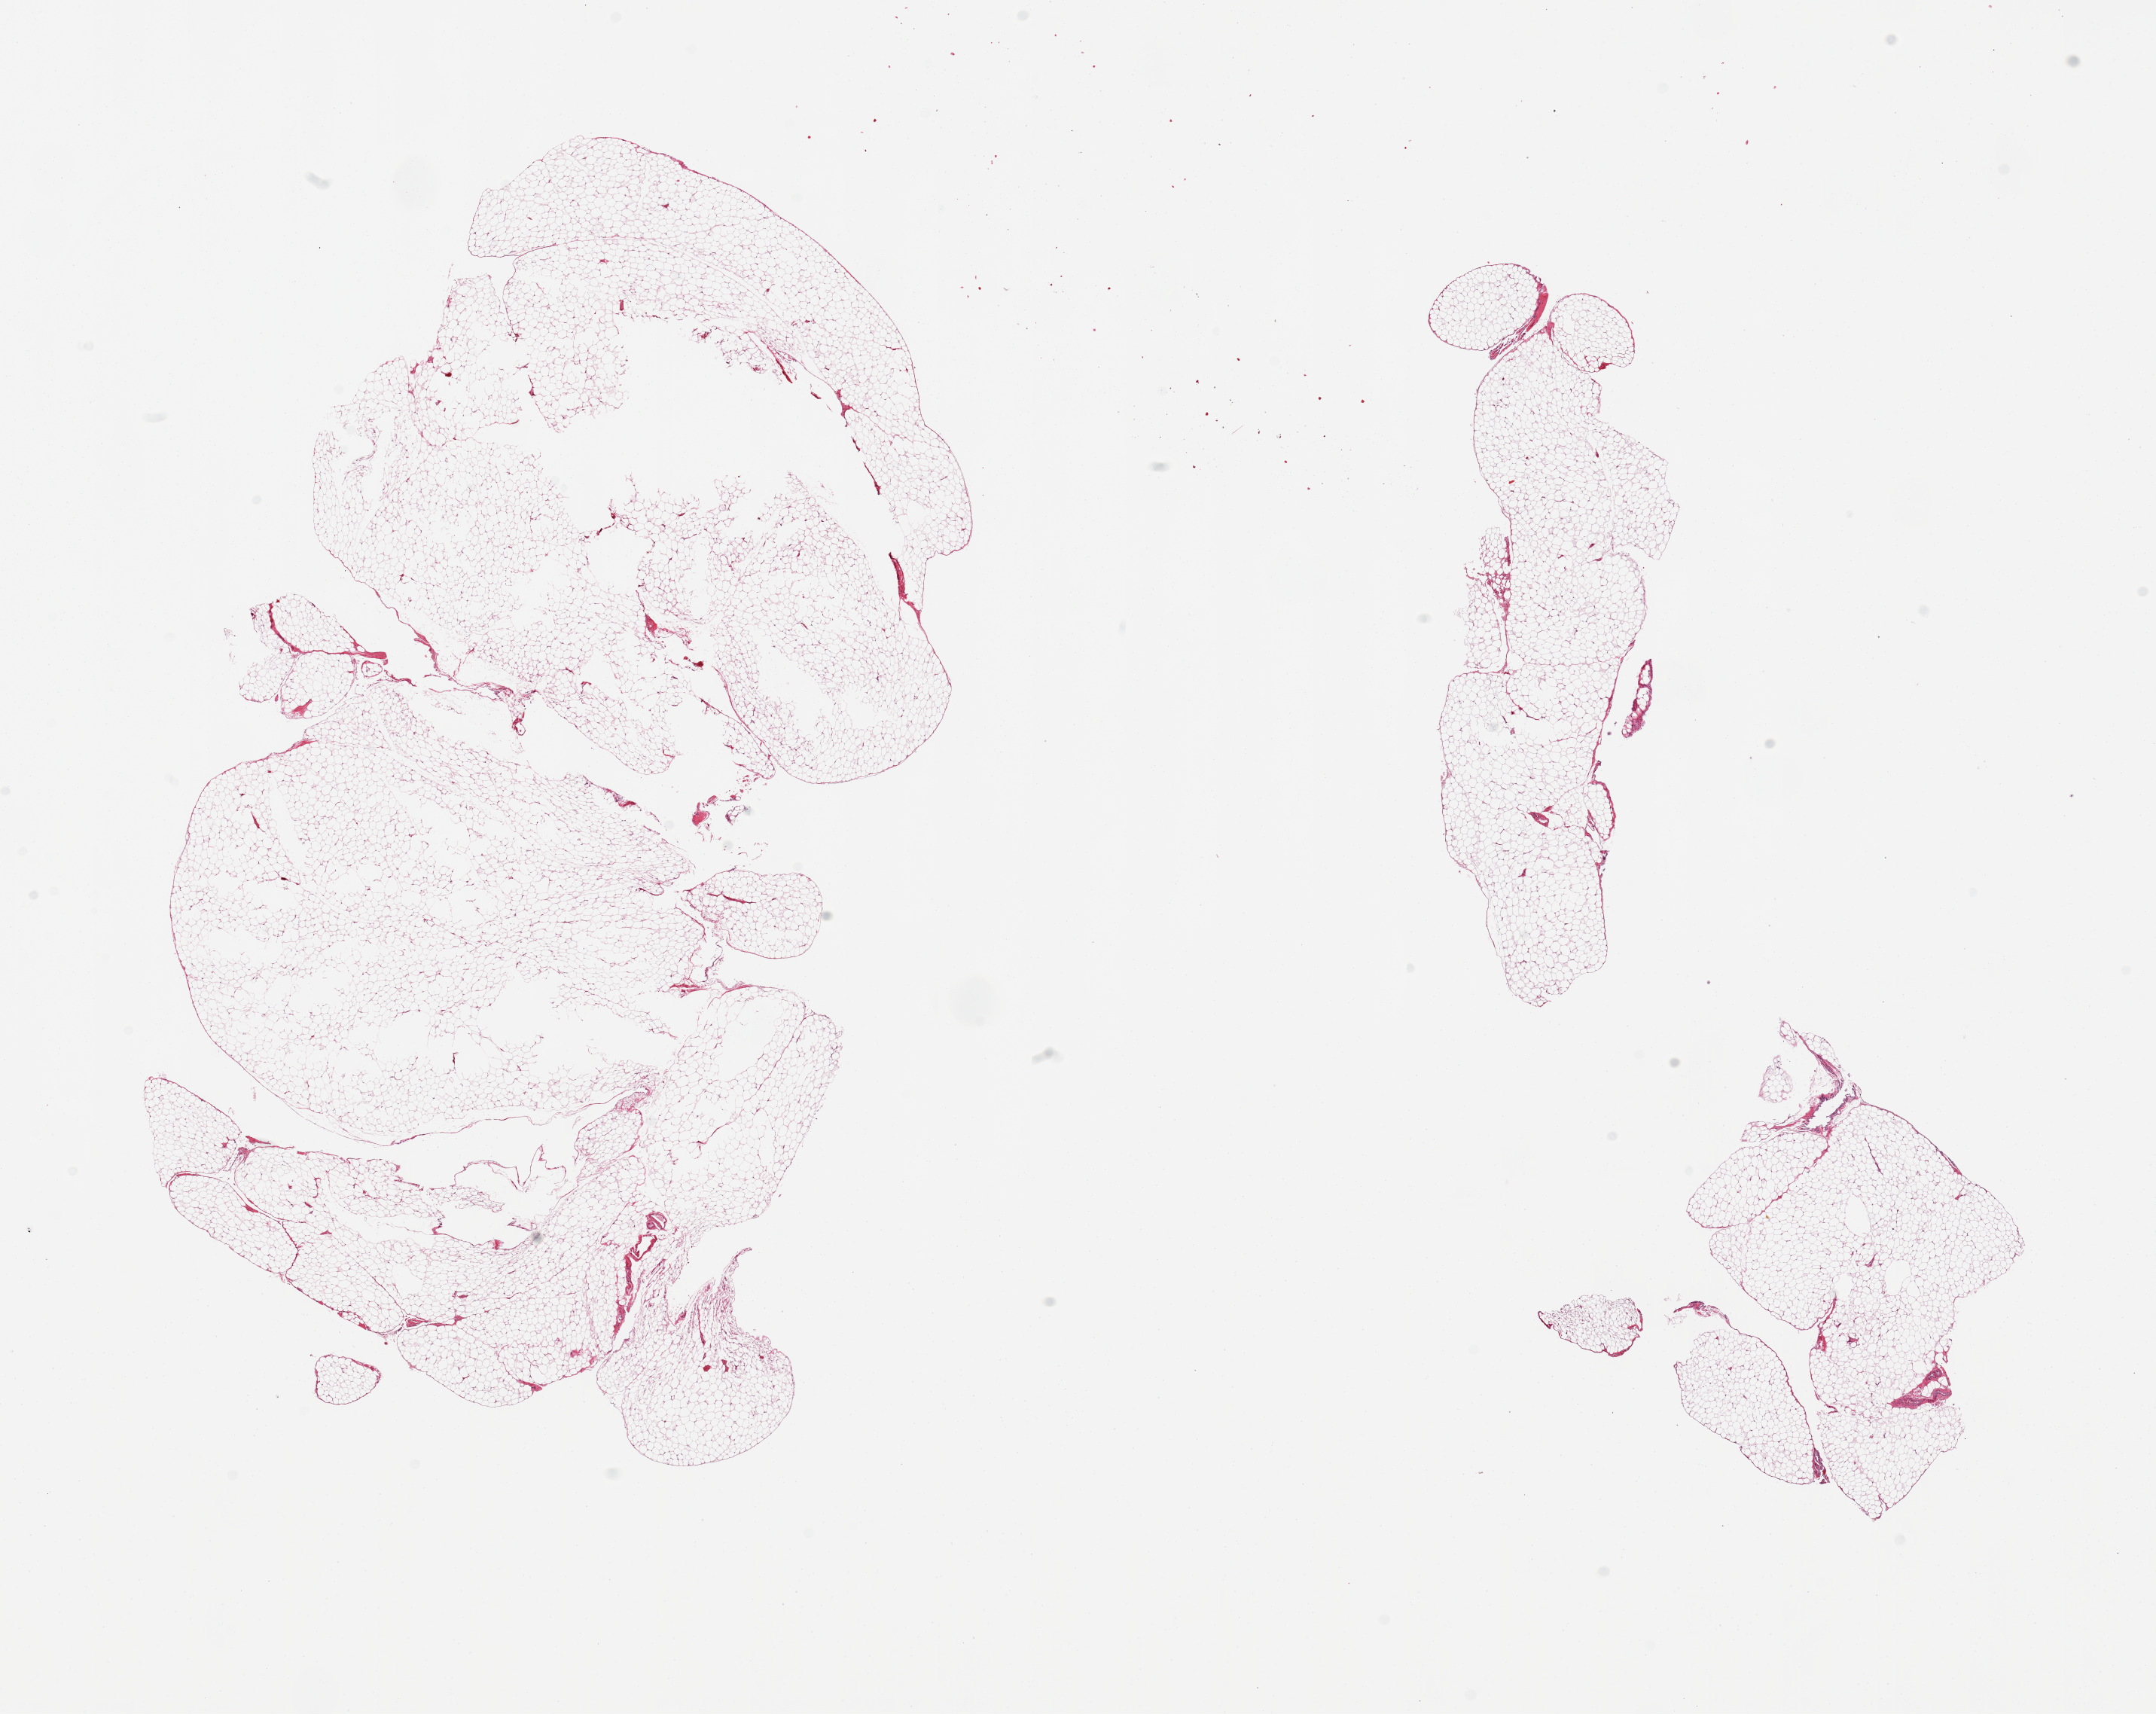
H&E whole-slide image — a low-resolution overview of the entire scanned area, about 22.6 x 18.0 mm, PAXgene-fixed, paraffin-embedded tissue, target tissue: omentum, donor tissue sample. Donor sex: male.
Pathologist's review note for this sample: 2 pieces, minimal-no vascular tissue/fibrosis.